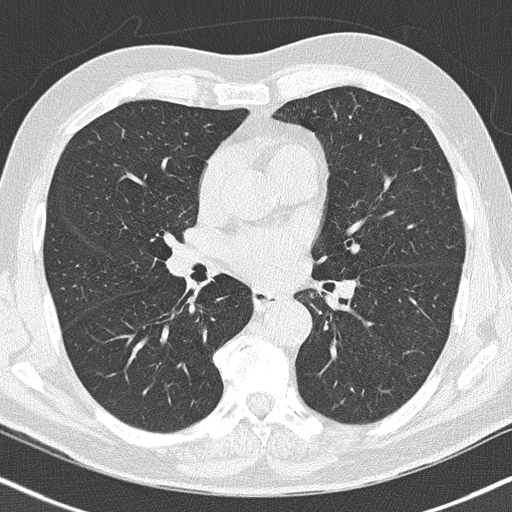
Axial slice from a low-dose chest CT screening exam; baseline screening round; lung window (W 1500 / L -600 HU); 2 mm slice thickness; slice 89 of 186 in the series; 512 × 512 image matrix. Male, age 66 years at enrolment. Current smoker at enrolment.
Lesion marked by an expert reader, box from (x=185, y=272) to (x=206, y=296) px. Reader record for this screening exam (exam-level; its link to the box is not recorded): non-calcified nodule or mass ≥4 mm, right upper lobe, 5 × 4 mm, smooth margins. Official screen result: positive, change unspecified: nodule(s) >= 4 mm or enlarging nodule(s), mass(es), or other non-specific abnormalities suspicious for lung cancer. Lung cancer was diagnosed 778 days after this screen (after the third annual screen): squamous cell carcinoma, NOS, right lower lobe, poorly differentiated (G3), stage IIA (AJCC 6th edition), 22 mm at pathology.